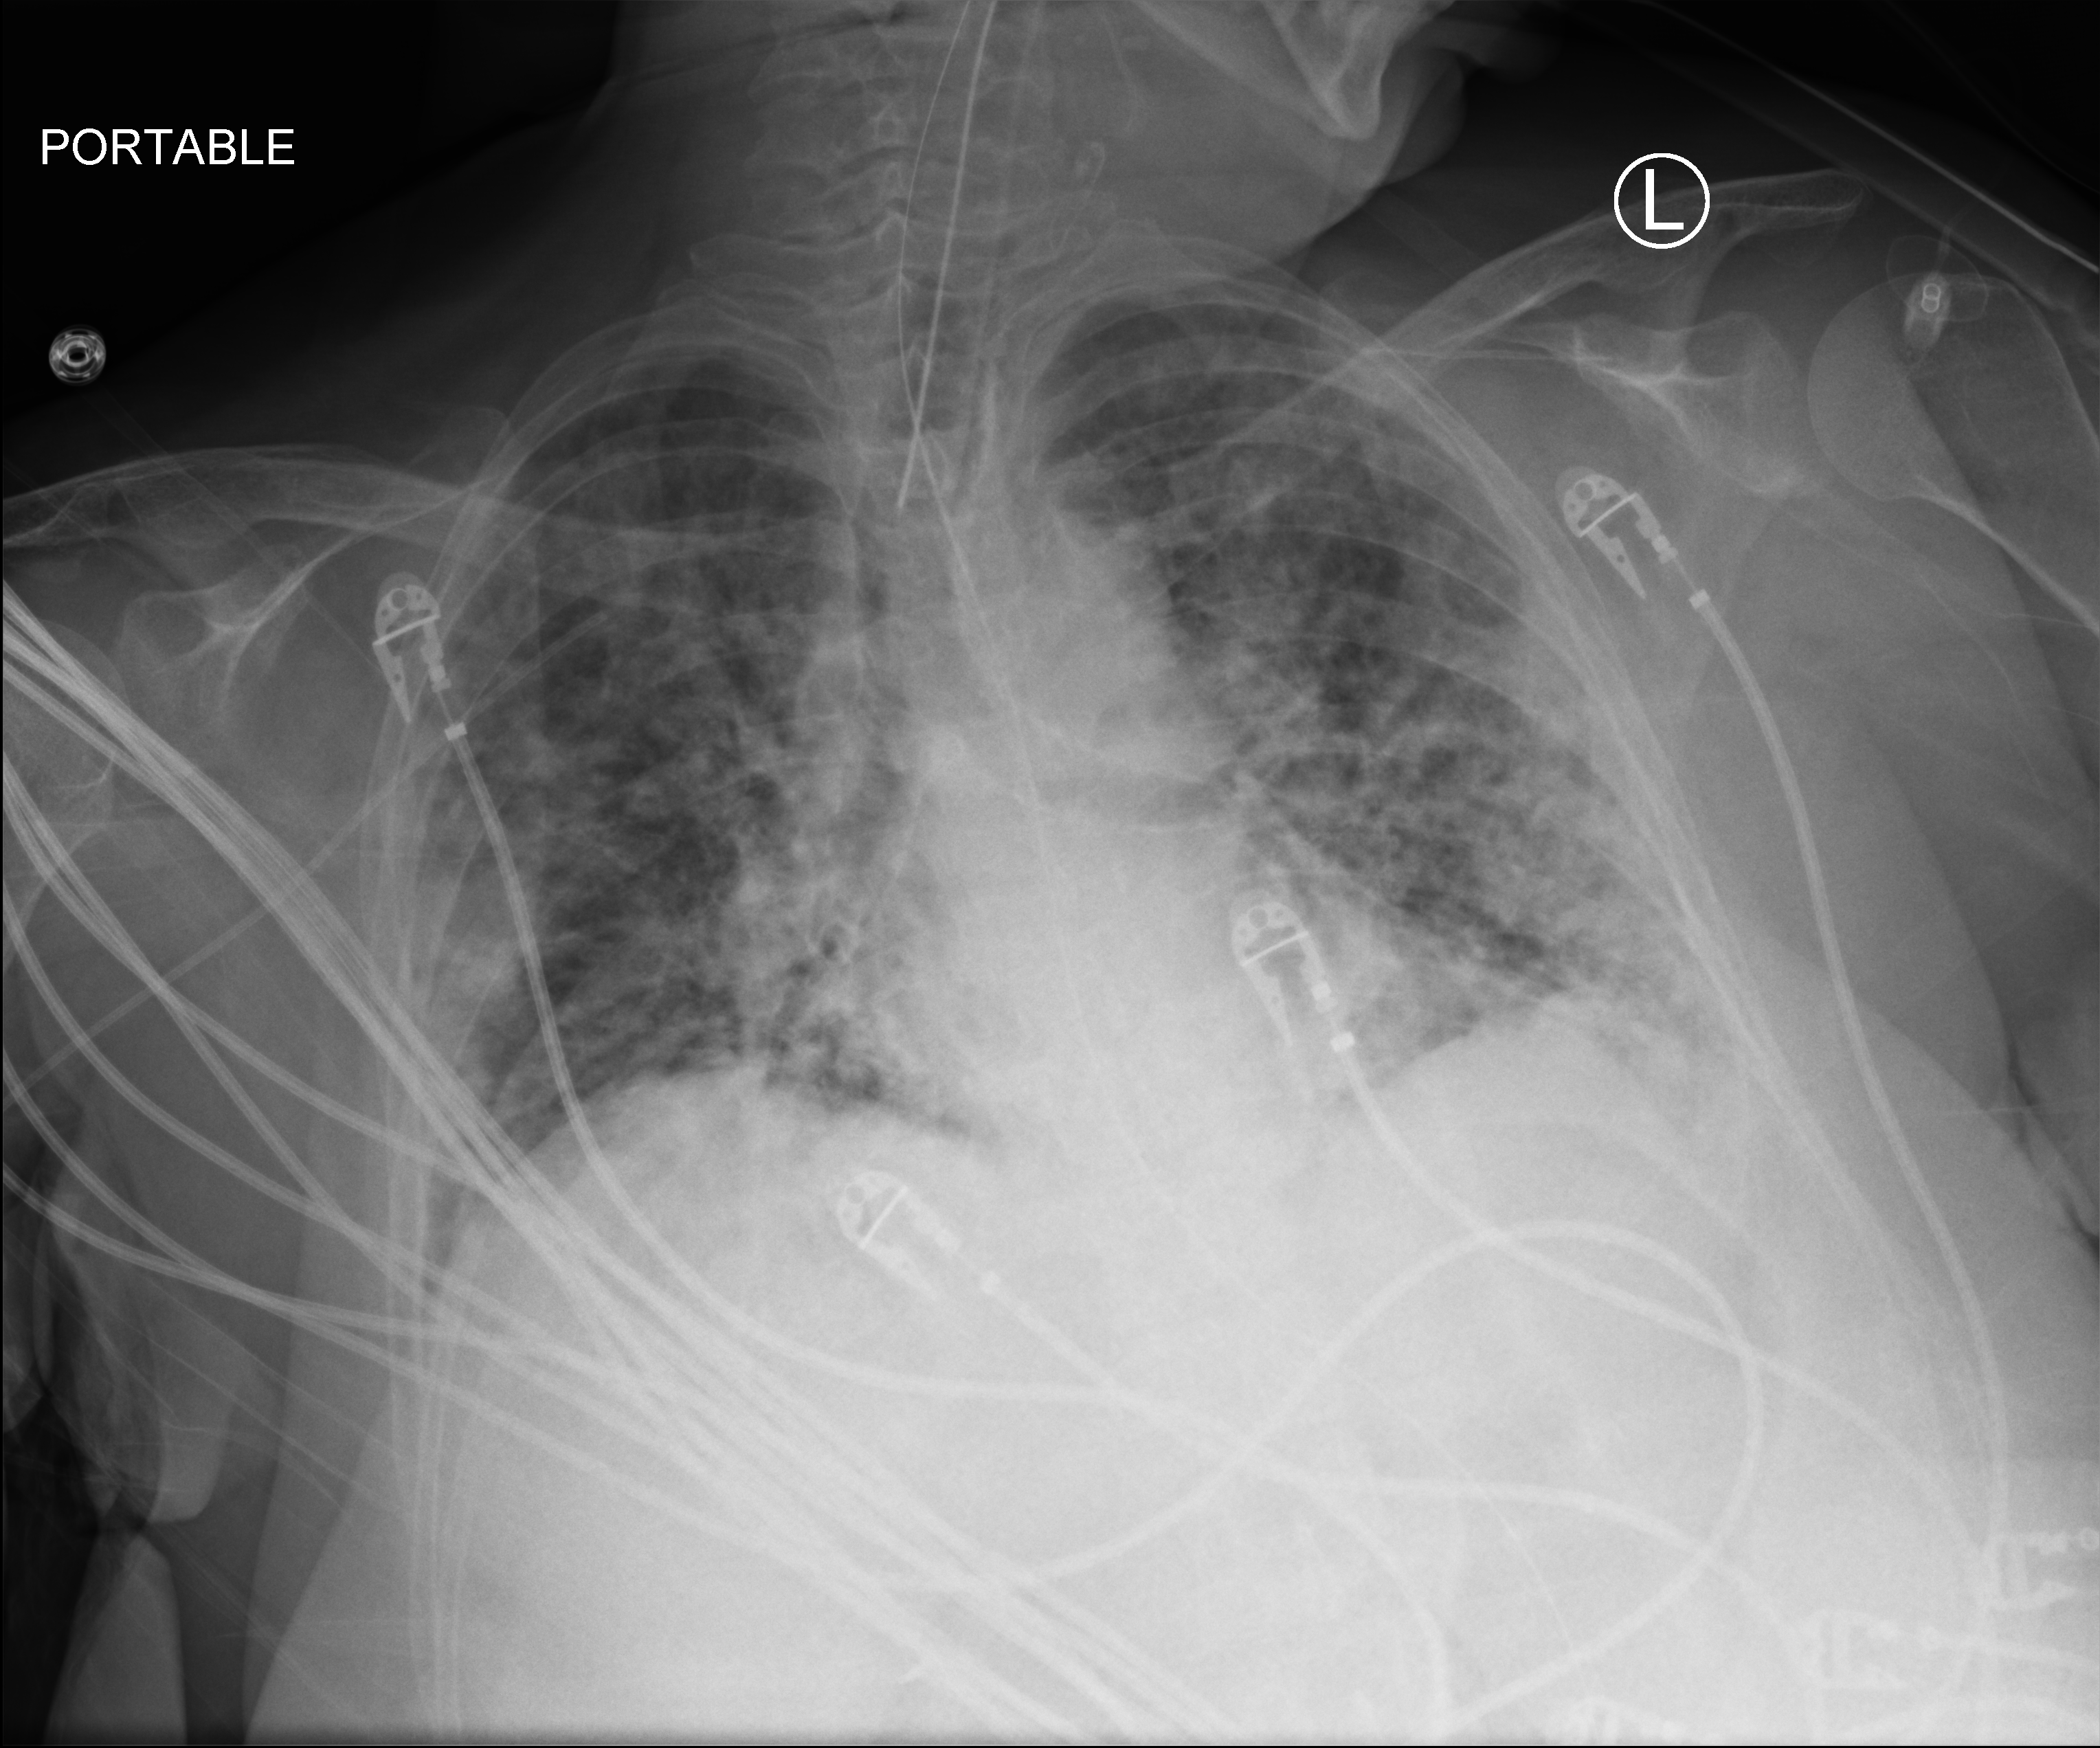
Chest X-ray (portable); anteroposterior (AP) projection. Female patient hospitalised with COVID-19, age 18–59 years.
Hospital-stay facts (about this admission, not read from this image; timing relative to this image not recorded):
- mechanically ventilated during this hospital stay: yes
- admitted to intensive care during this hospital stay: yes